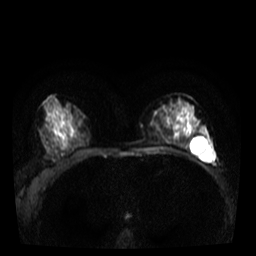
Breast MRI, one axial slice. Slice 18 of 40 in the series (ordered by position). Diffusion-weighted series; image 2 of 4 stored at this slice position (different b-values; order by instance number). 3 T. 5 mm slice thickness. 256 × 256 image matrix, field of view 320 × 320 mm. Female patient.
Structures marked on this image (manually delineated by an expert):
- tumour on diffusion-weighted imaging: bounding box [x1, y1, x2, y2] px = [198, 150, 214, 161]